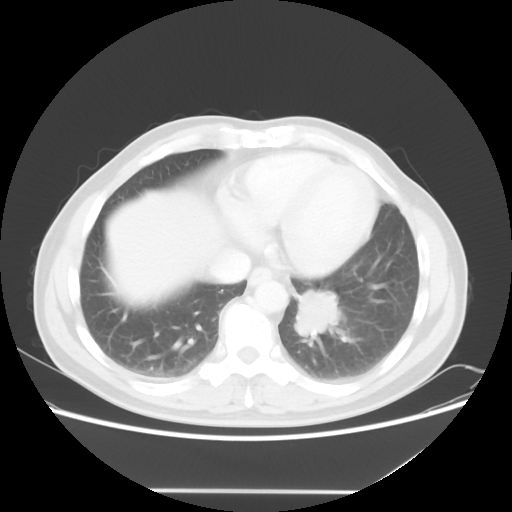
Chest CT, one axial slice. Slice 17 of 56 in the series (ordered by position). Reconstruction kernel STANDARD. Lung window (W 1500 / L -600 HU). 5 mm slice thickness. 512 × 512 image matrix, field of view 385 × 385 mm. Patient: male, 61 years. Case-level facts recorded for this patient, not image findings: clinical TNM (as recorded): T1c N0 M0.
Structures marked on this image (bounding box drawn by a radiologist):
- lung tumour (recorded histology: adenocarcinoma): box from (x=292, y=284) to (x=350, y=350) px